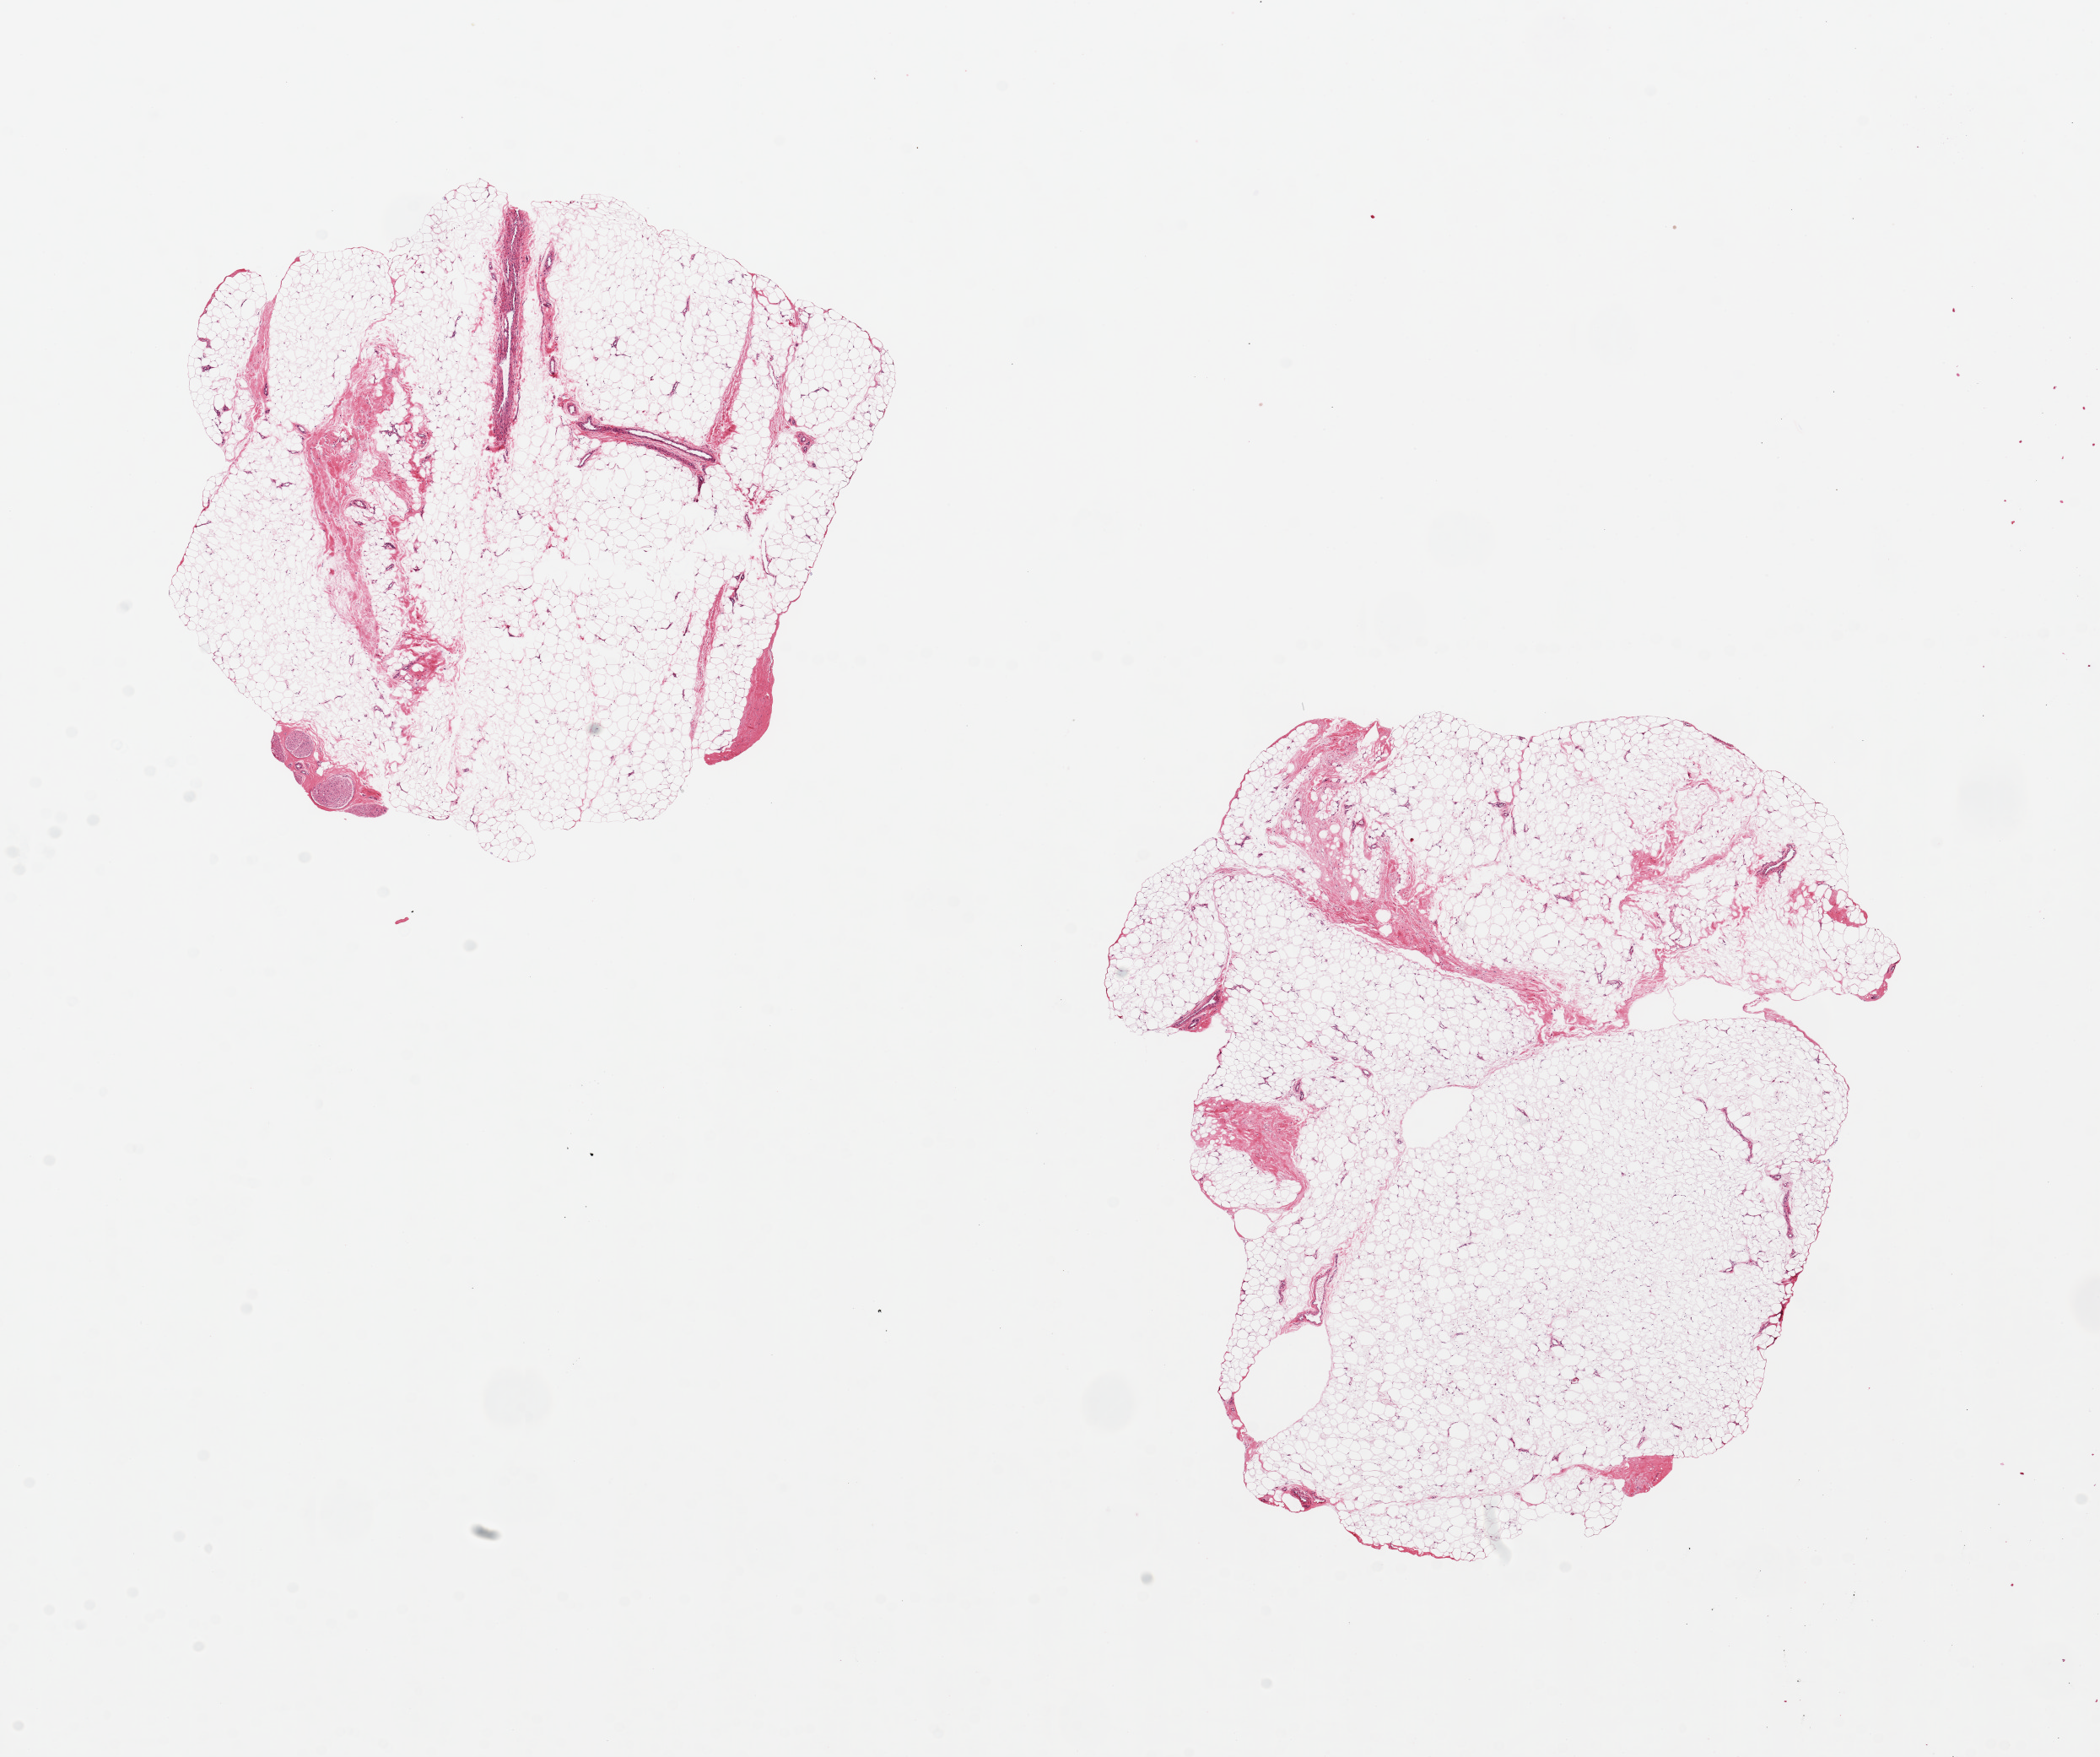
Digitized haematoxylin and eosin-stained section — shown as a low-resolution overview of the whole scanned area (about 19.7 x 16.5 mm, acquisition: 20x scan); PAXgene-fixed paraffin-embedded (PFPE) section; section of adipose tissue (target tissue); tissue donor sample. Male donor.
Review note (as recorded): 2 pieces ~7x6mm.